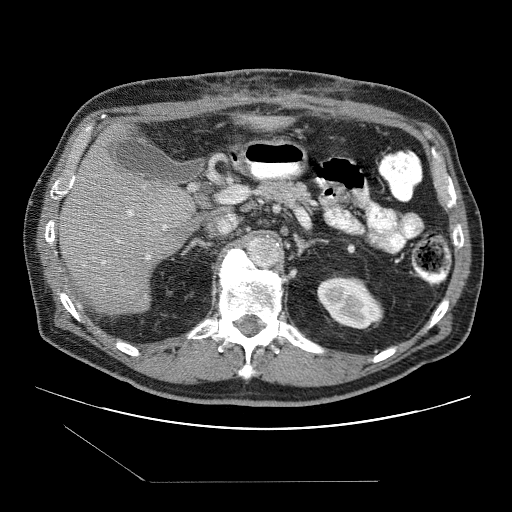
Contrast-enhanced abdominal CT (liver protocol), one axial slice. Slice 51 of 109 in the series (ordered by position). One of 2 acquisitions stored at this slice position. Soft-tissue window (W 400 / L 40 HU). 512 × 512 image matrix, field of view 400 × 400 mm. Case-level facts recorded for this patient, not image findings: diagnosis: hepatocellular carcinoma (patient treated with transarterial chemoembolisation; whether this scan precedes or follows treatment is not stated here); TNM stage (as recorded): Stage-IIIB; Child-Pugh class: A; tumour nodularity: multinodular.
Structures marked on this image (semi-automatic segmentation, software-assisted and operator-edited):
- liver parenchyma outside the tumour (the mass and vessels are separate outlines, so this box may not span the whole liver): box from (x=56, y=122) to (x=194, y=312) px
- liver vessels: (x=102, y=210)–(x=167, y=264)